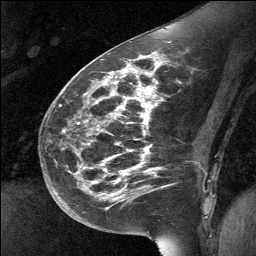
Breast MRI (dynamic contrast-enhanced), one sagittal slice; slice 29 of 64 in the series (ordered by position); dynamic contrast-enhanced study with each time point stored as its own series, time point 2 of 3 at this slice position (early post-contrast, ordered by acquisition time); 1.5 T; TE 4.8 ms, TR 27 ms; 256 × 256 image matrix, field of view 200 × 200 mm. Patient: female, 39 years. Case-level facts recorded for this patient, not image findings: setting: breast cancer imaged before/during neoadjuvant chemotherapy; receptor status: HER2-positive.
Structures marked on this image (semi-automatically segmented with operator editing):
- analysis volume of interest (the breast-tissue region the enhancement analysis was run in; not a lesion): bounding box (x1, y1, x2, y2) in pixels: (70, 69, 159, 224)
- tumour enhancement mask (voxels above the 90 % enhancement threshold inside the analysis volume of interest): (112, 69, 133, 195)